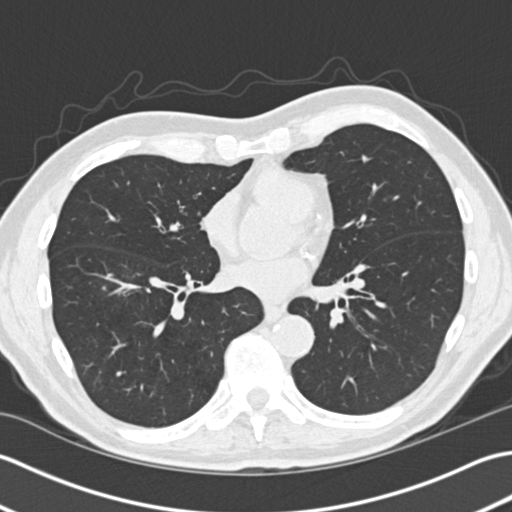
Low-dose screening chest CT, one axial slice. Position 75 of 172 along the scan axis. 120 kVp. Lung window (W 1500 / L -600 HU). 2 mm slice thickness. 512 × 512 image matrix.
Structures marked on this image (outlined manually by an expert reader):
- lesion 1 (tumor, lower lobe of right lung): bounding box <104,278,141,288> (left, top, right, bottom; pixels)